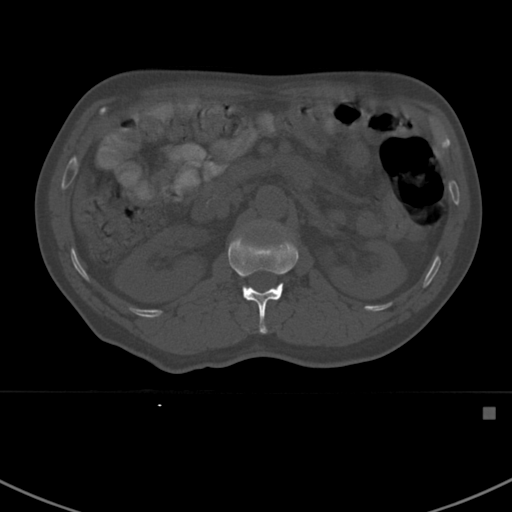
CT including the spine, one axial slice. Slice 305 of 412 in the series (ordered by position). Reconstruction kernel Br40s. 120 kVp. Bone window (W 1800 / L 400 HU). 1.5 mm slice thickness. 512 × 512 image matrix, field of view 358 × 358 mm. Patient: male, 59 years. Case-level facts recorded for this patient, not image findings: primary cancer: prostate.
Structures marked on this image (semi-automatically segmented with operator editing):
- L1 vertebra: bounding box [x1, y1, x2, y2] px = [228, 233, 299, 334]